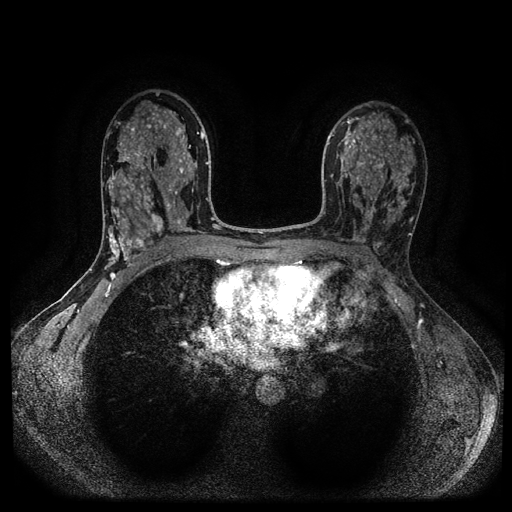
Breast MRI (dynamic contrast-enhanced, multi-phase), one axial slice; slice 62 of 116 in the series (ordered by position); dynamic contrast-enhanced series, time point 2 of 5 at this slice position (early post-contrast); 1.5 T; TE 2.6 ms, TR 5.4 ms; 2 mm slice thickness; 512 × 512 image matrix, field of view 340 × 340 mm. Patient: female, 43 years.
Structures marked on this image (semi-automatically segmented with operator editing):
- breast lesion (labelled benign in the annotation): bounding box <150,213,165,237> (left, top, right, bottom; pixels)